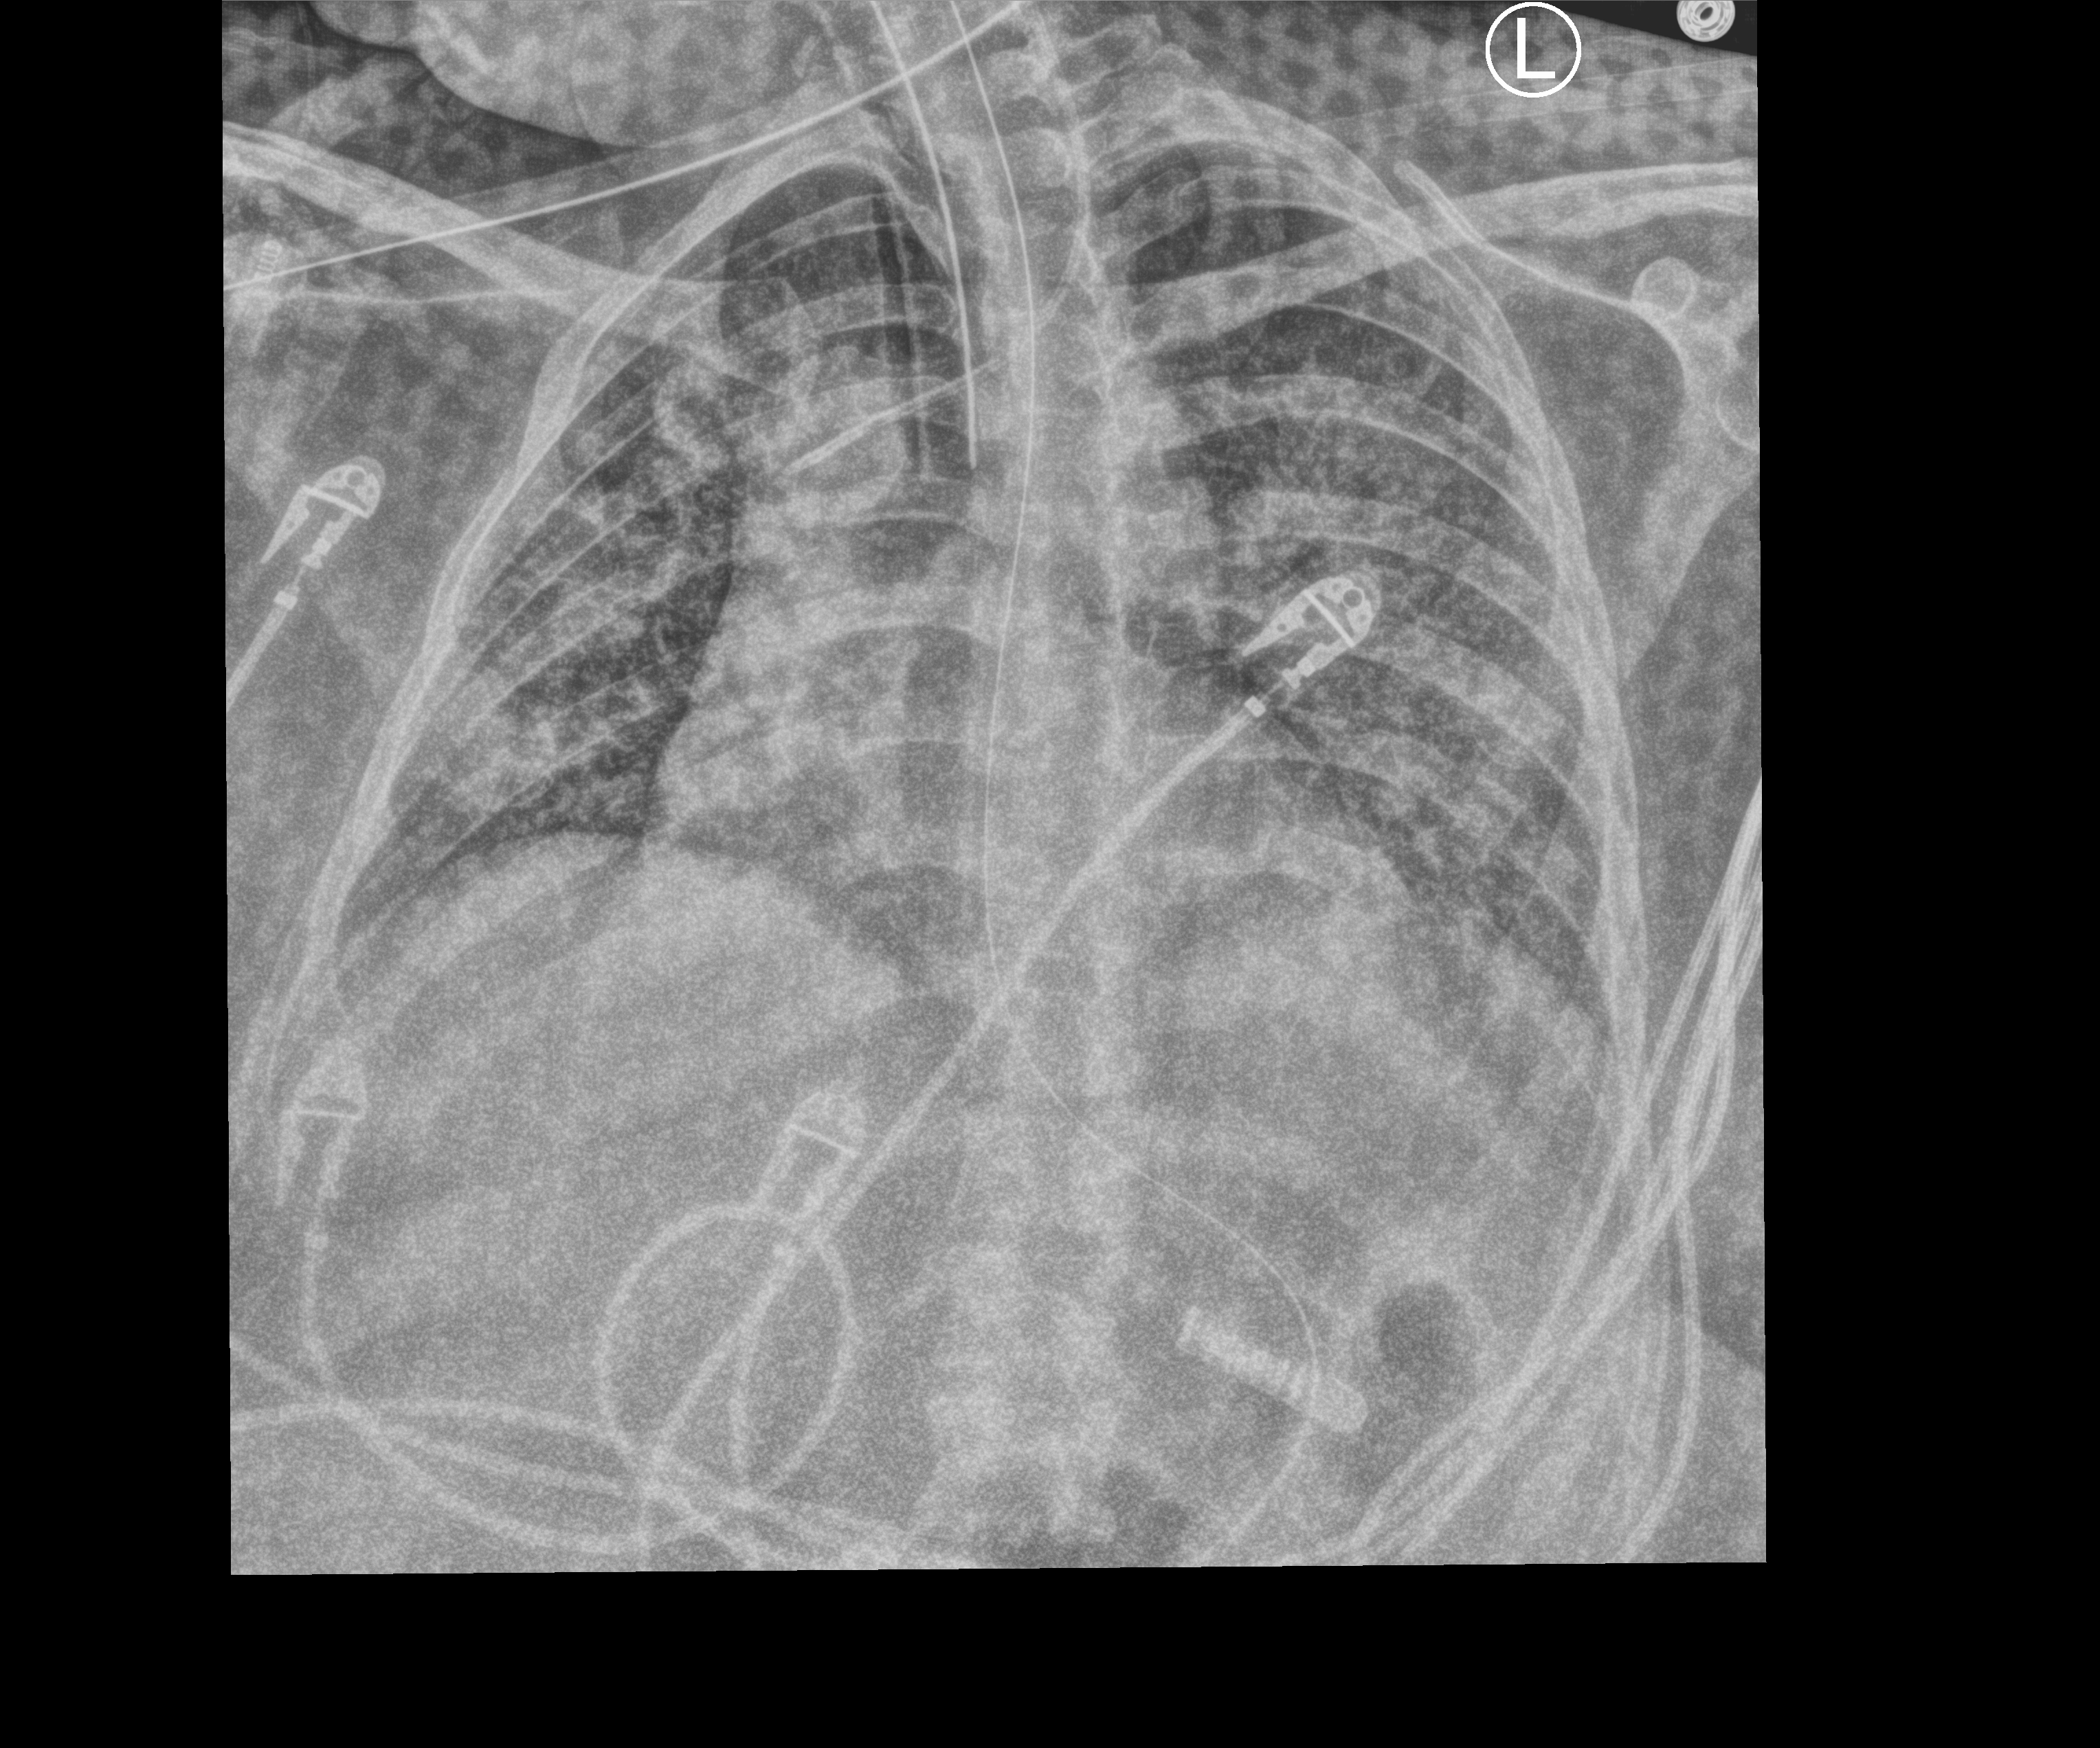
Bedside chest radiograph (computed radiography), anteroposterior (AP) projection. Patient hospitalised with COVID-19; female, aged 18–59 years.
Hospital-stay facts (about this admission, not read from this image; timing relative to this image not recorded): mechanically ventilated during this hospital stay: yes.